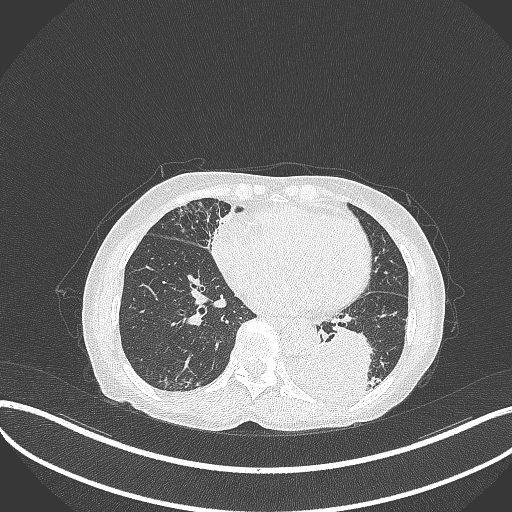
Chest CT, one axial slice; slice 109 of 370 in the series (ordered by position); lung window (W 1500 / L -600 HU); 512 × 512 image matrix, field of view 400 × 400 mm. Patient: female, 78 years. Case-level facts recorded for this patient, not image findings: clinical TNM (as recorded): T3 N0 M1.
Structures marked on this image (rectangle marked by the reading radiologist):
- lung tumour (recorded histology: squamous cell carcinoma): bounding box [x1, y1, x2, y2] px = [283, 323, 370, 410]